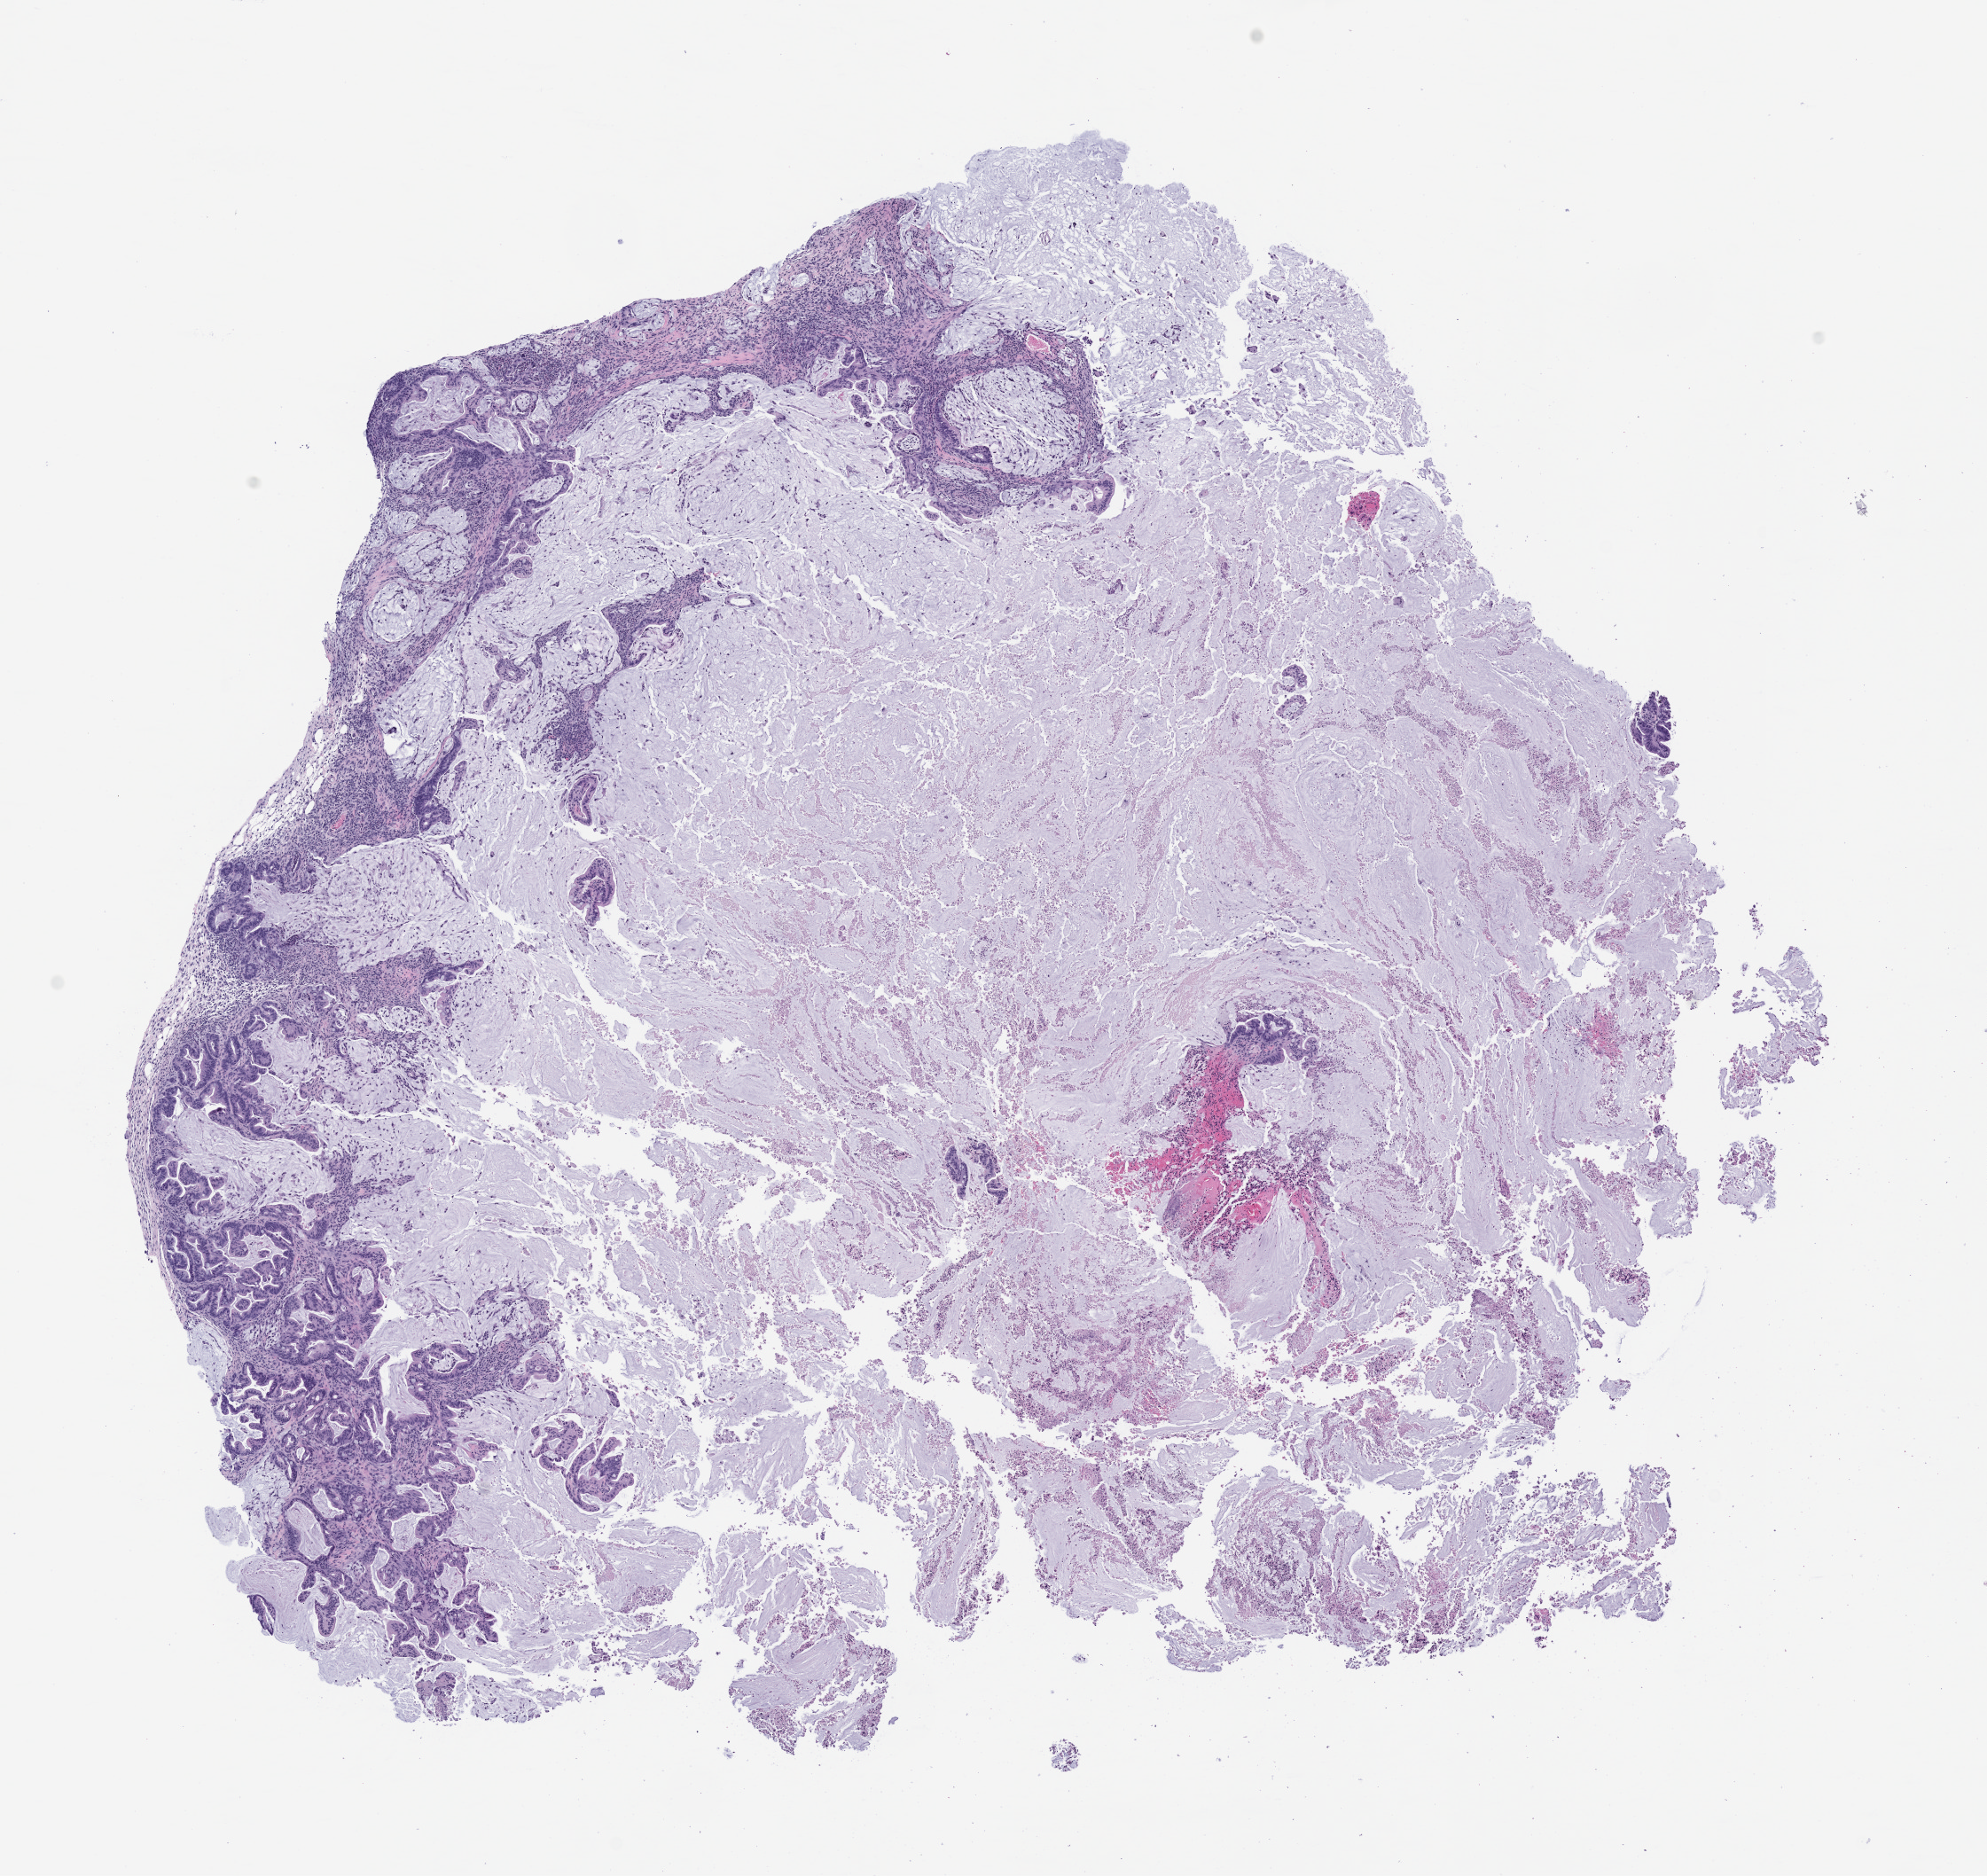
Whole-slide image, haematoxylin and eosin: patient-derived xenograft (human tumor grown in a mouse), passage 1, low-resolution overview of the scanned area, about 9.0 x 8.5 mm. Formalin-fixed, paraffin-embedded (FFPE) tissue. Originating tumor site category: rectum.
• originating patient diagnosis: Rectal Adenocarcinoma